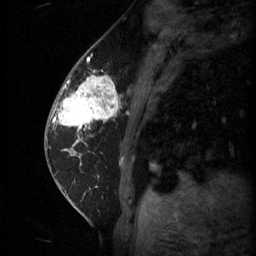
Breast MRI (dynamic contrast-enhanced), one sagittal slice. Slice 19 of 60 in the series (ordered by position). 3 images stored at this slice position (order not interpretable as contrast timing). 1.5 T. TE 4.2 ms, TR 11 ms. 2 mm slice thickness. 256 × 256 image matrix, field of view 180 × 180 mm. Female patient, age 62 years.
Annotated regions visible in this slice (semi-automatic segmentation, software-assisted and operator-edited):
- analysis volume of interest (the breast-tissue region the enhancement analysis was run in; not a lesion): bounding box <55,72,124,135> (left, top, right, bottom; pixels)
- tumour enhancement mask (voxels above the 70 % enhancement threshold inside the analysis volume of interest): <55,76,119,131>